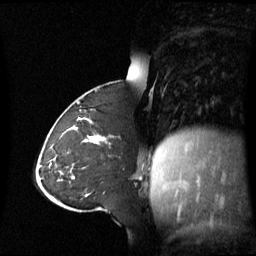
Breast MRI (dynamic contrast-enhanced), one sagittal slice; slice 26 of 60 in the series (ordered by position); dynamic contrast-enhanced series, image 2 of 3 at this slice position (ordered by acquisition); 1.5 T; TE 4.2 ms, TR 8.4 ms; 2.8 mm slice thickness; 256 × 256 image matrix, field of view 270 × 270 mm. Patient: female, 43 years. From the clinical record (not read from this slice): setting: breast cancer imaged before/during neoadjuvant chemotherapy; receptor status: triple-negative.
Structures marked on this image (semi-automatic segmentation, software-assisted and operator-edited):
- analysis volume of interest (the breast-tissue region the enhancement analysis was run in; not a lesion): bounding box (x1, y1, x2, y2) in pixels: (55, 124, 110, 173)
- tumour enhancement mask (voxels above the 70 % enhancement threshold inside the analysis volume of interest): (88, 135, 105, 144)